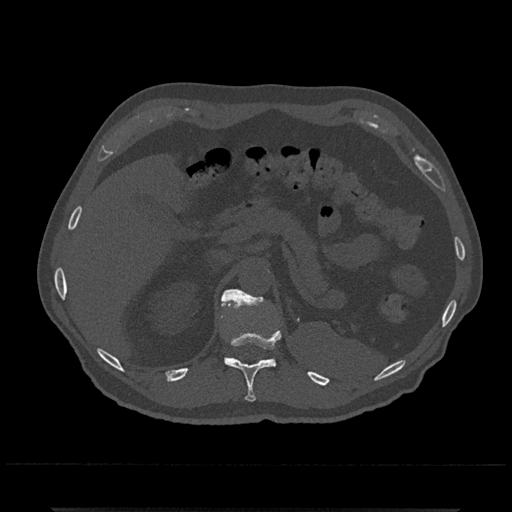
CT including the spine, one axial slice; slice 473 of 797 in the series (ordered by position); reconstruction kernel Br40s/3; 120 kVp; bone window (W 1800 / L 400 HU); 0.5 mm slice thickness; 512 × 512 image matrix, field of view 393 × 393 mm. Male patient, age 67 years. From the clinical record (not read from this slice): primary cancer: prostate.
Annotated regions visible in this slice (semi-automatic segmentation, software-assisted and operator-edited):
- T11 vertebra: box from (x=221, y=301) to (x=281, y=402) px
- T12 vertebra: (x=222, y=289)–(x=268, y=359)